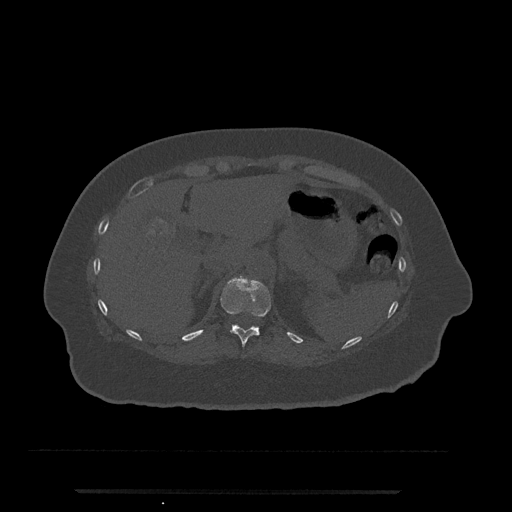
CT including the spine, one axial slice; slice 220 of 797 in the series (ordered by position); reconstruction kernel Br40s/3; 120 kVp; bone window (W 1800 / L 400 HU); 512 × 512 image matrix, field of view 440 × 440 mm. Patient: female, 51 years. From the clinical record (not read from this slice): primary cancer: neuro; vertebrae with lytic lesions (as recorded): T8.
Outlined on this slice (semi-automatic segmentation, software-assisted and operator-edited):
- T11 vertebra: box from (x=220, y=275) to (x=271, y=347) px